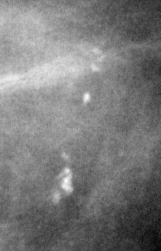
Crop from a digitized film mammogram around one marked abnormality; right breast; MLO view.
Marked abnormality: calcifications, morphology pleomorphic, distribution linear; BI-RADS assessment category 4; subtlety rating 4 on a 1 (subtle) to 5 (obvious) scale; pathology (as recorded): malignant.